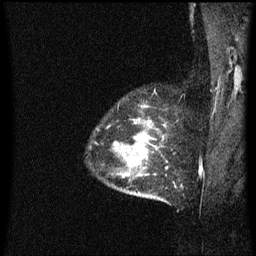
Breast MRI (dynamic contrast-enhanced), one sagittal slice. Slice 51 of 60 in the series (ordered by position). Dynamic contrast-enhanced series, image 2 of 3 at this slice position (ordered by acquisition). 1.5 T. TE 4.2 ms, TR 8.4 ms. 256 × 256 image matrix, field of view 200 × 200 mm. Patient: female, 34 years. Case-level facts recorded for this patient, not image findings: setting: breast cancer imaged before/during neoadjuvant chemotherapy; receptor status: HR-positive, HER2-negative.
Structures marked on this image (semi-automatic segmentation, software-assisted and operator-edited):
- analysis volume of interest (the breast-tissue region the enhancement analysis was run in; not a lesion): box from (x=110, y=120) to (x=169, y=203) px
- tumour enhancement mask (voxels above the 70 % enhancement threshold inside the analysis volume of interest): (x=136, y=136)–(x=153, y=153)